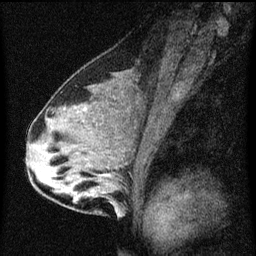
Breast MRI (dynamic contrast-enhanced), one sagittal slice. Position 34 of 60 along the scan axis. Dynamic contrast-enhanced series, image 2 of 3 at this slice position (ordered by acquisition). 1.5 T. TE 4.2 ms, TR 8 ms. 256 × 256 image matrix, field of view 180 × 180 mm. Patient: female, 33 years.
Annotated regions visible in this slice (semi-automatic segmentation, software-assisted and operator-edited):
- analysis volume of interest (the breast-tissue region the enhancement analysis was run in; not a lesion): bounding box (x1, y1, x2, y2) in pixels: (61, 126, 135, 213)
- tumour enhancement mask (voxels above the 70 % enhancement threshold inside the analysis volume of interest): (106, 174, 110, 177)